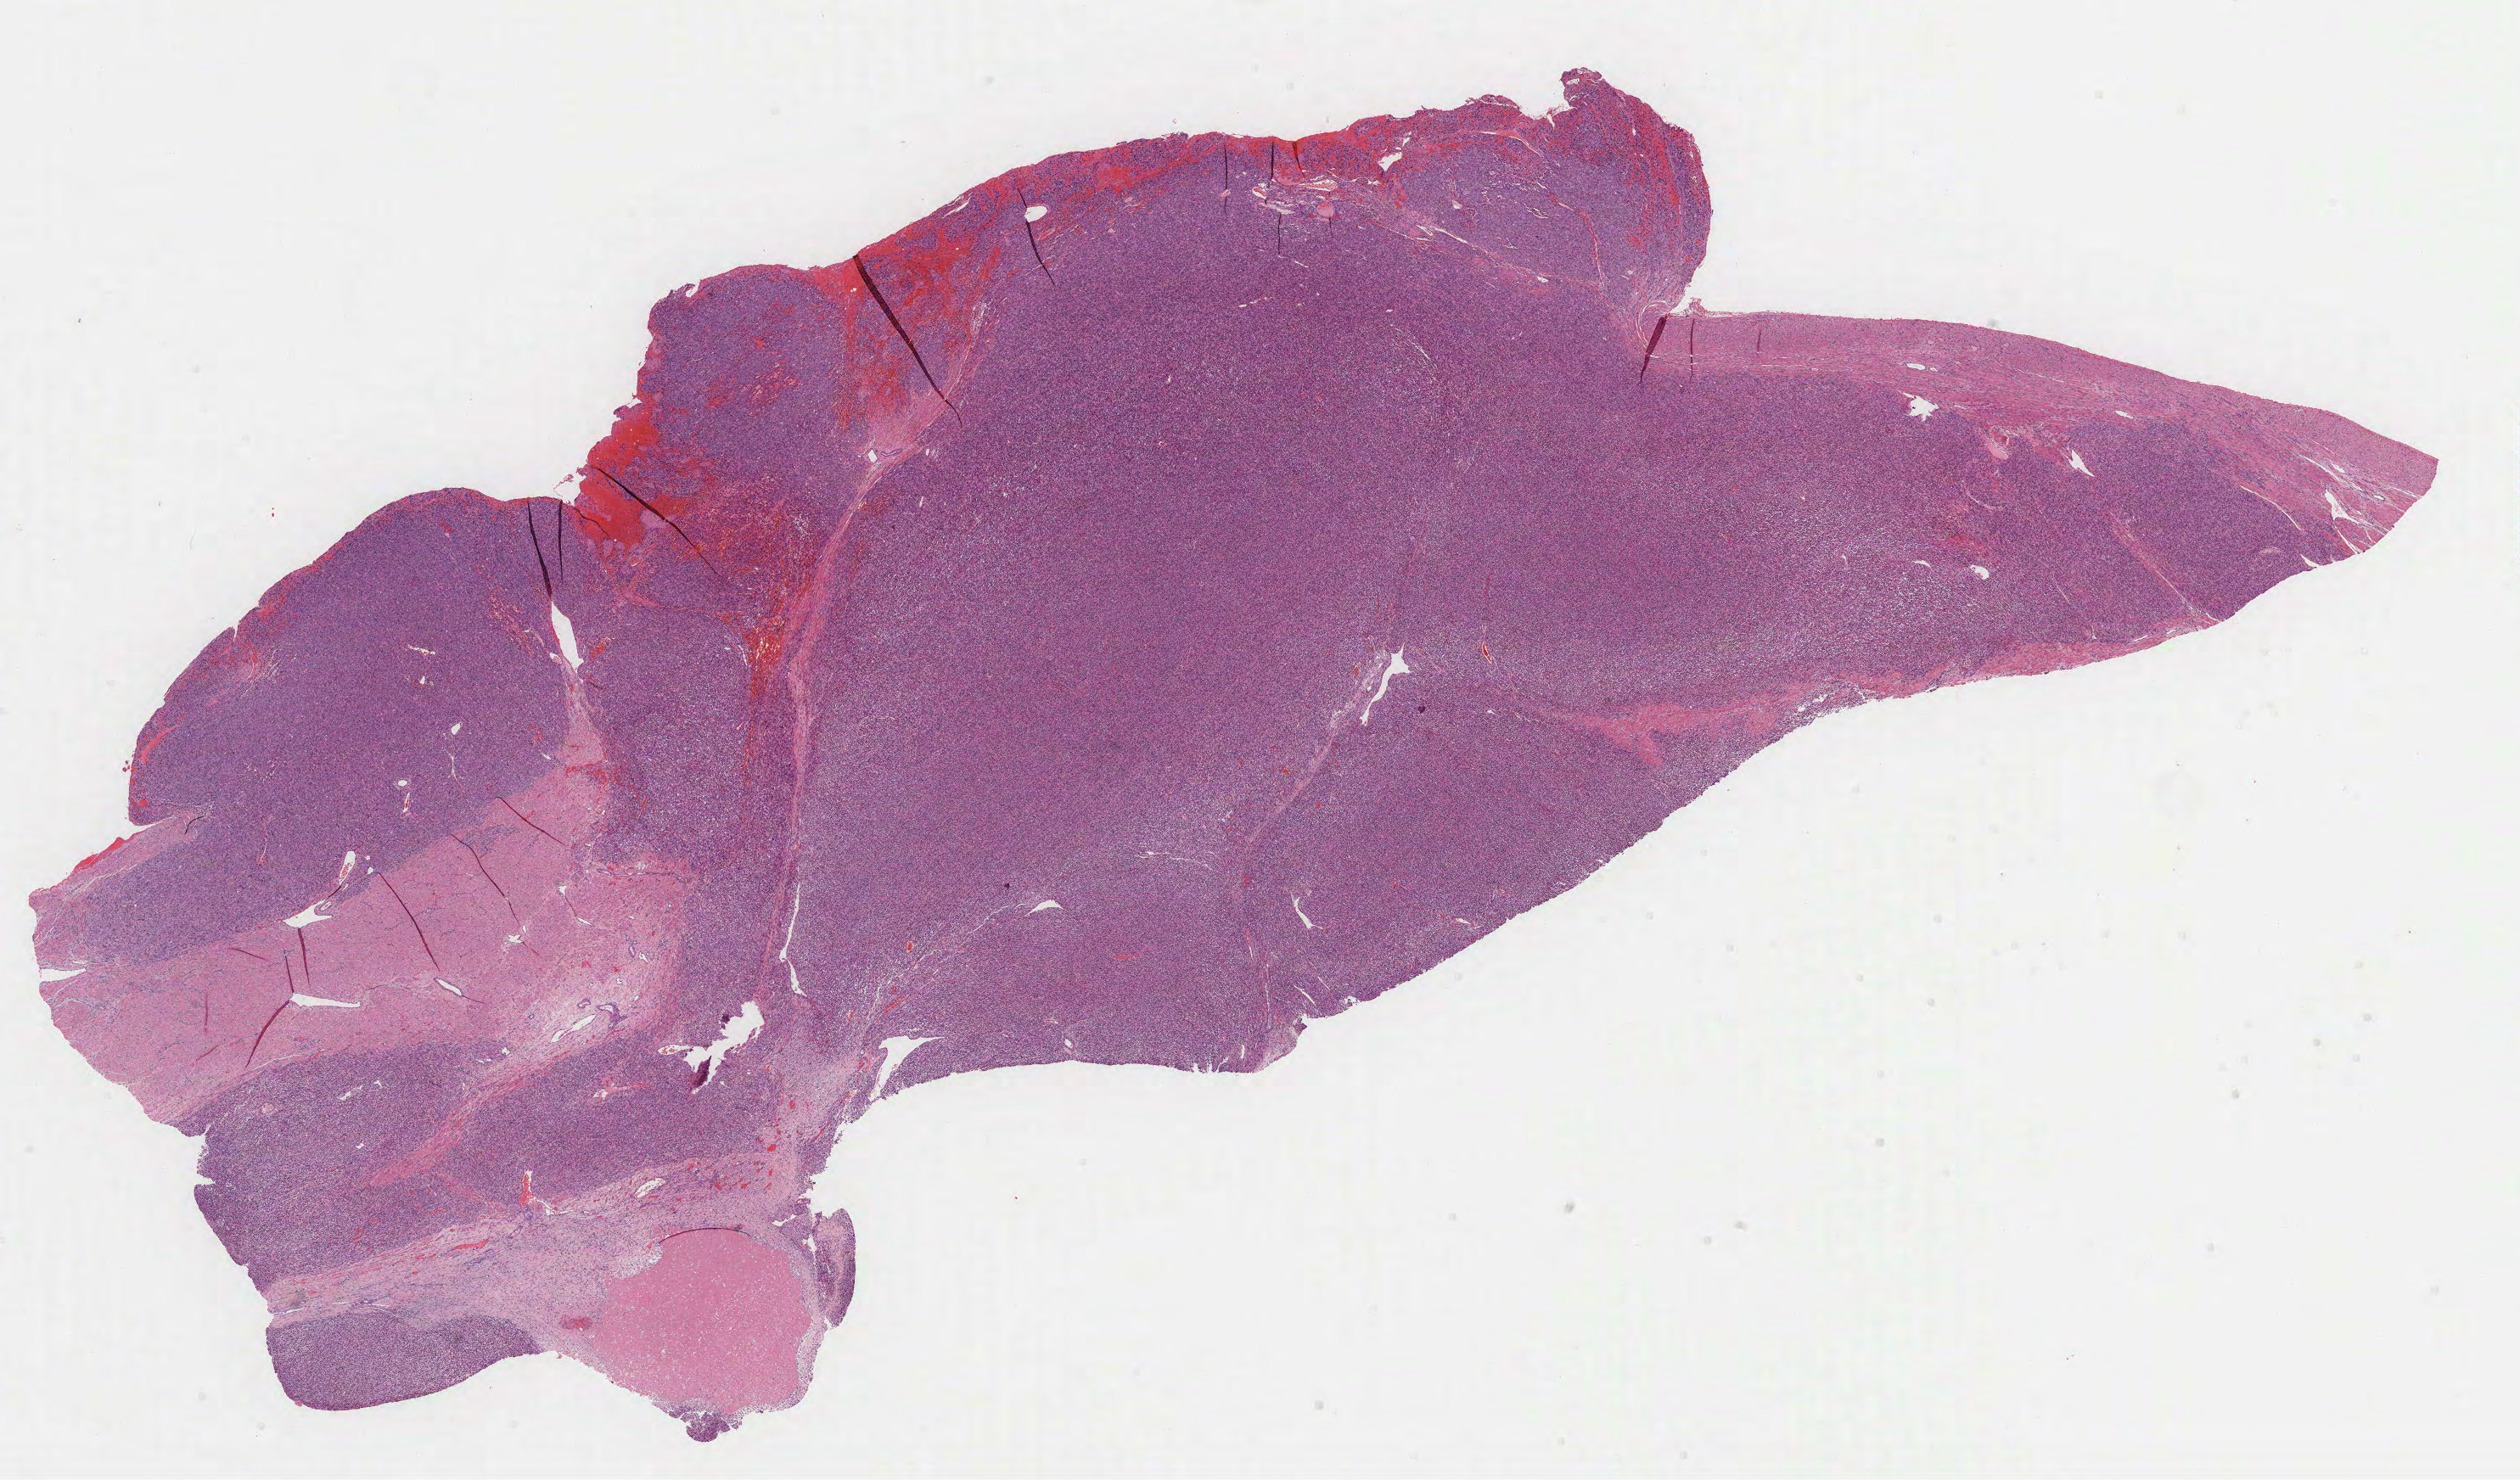
Whole-slide histology image, H&E-stained, low-resolution overview of the scanned area, about 24.0 x 14.1 mm (slide scanned at 40x); FFPE section; primary tumour sample from the uterus. Patient: female, age at initial diagnosis 48 years.
* diagnosis: Leiomyosarcoma, NOS